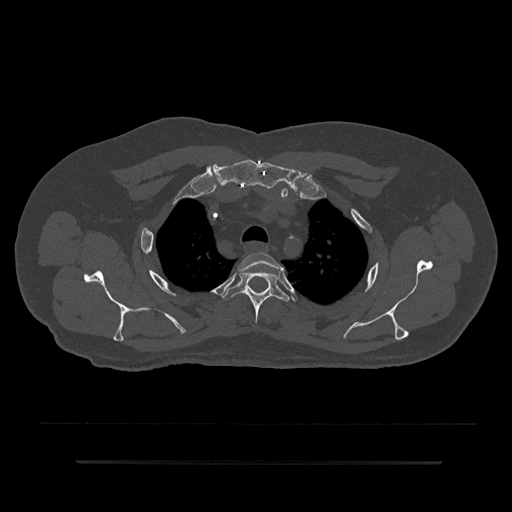
CT including the spine, one axial slice; position 667 of 797 along the scan axis; bone window (W 1800 / L 400 HU); 0.5 mm slice thickness; 512 × 512 image matrix, field of view 464 × 464 mm. Patient: male, 59 years. From the clinical record (not read from this slice): primary cancer: bile ducts; vertebrae with lytic lesions (as recorded): T10.
Outlined on this slice (semi-automatically segmented with operator editing):
- T2 vertebra: box from (x=238, y=252) to (x=281, y=291) px
- T3 vertebra: (x=223, y=269)–(x=289, y=324)